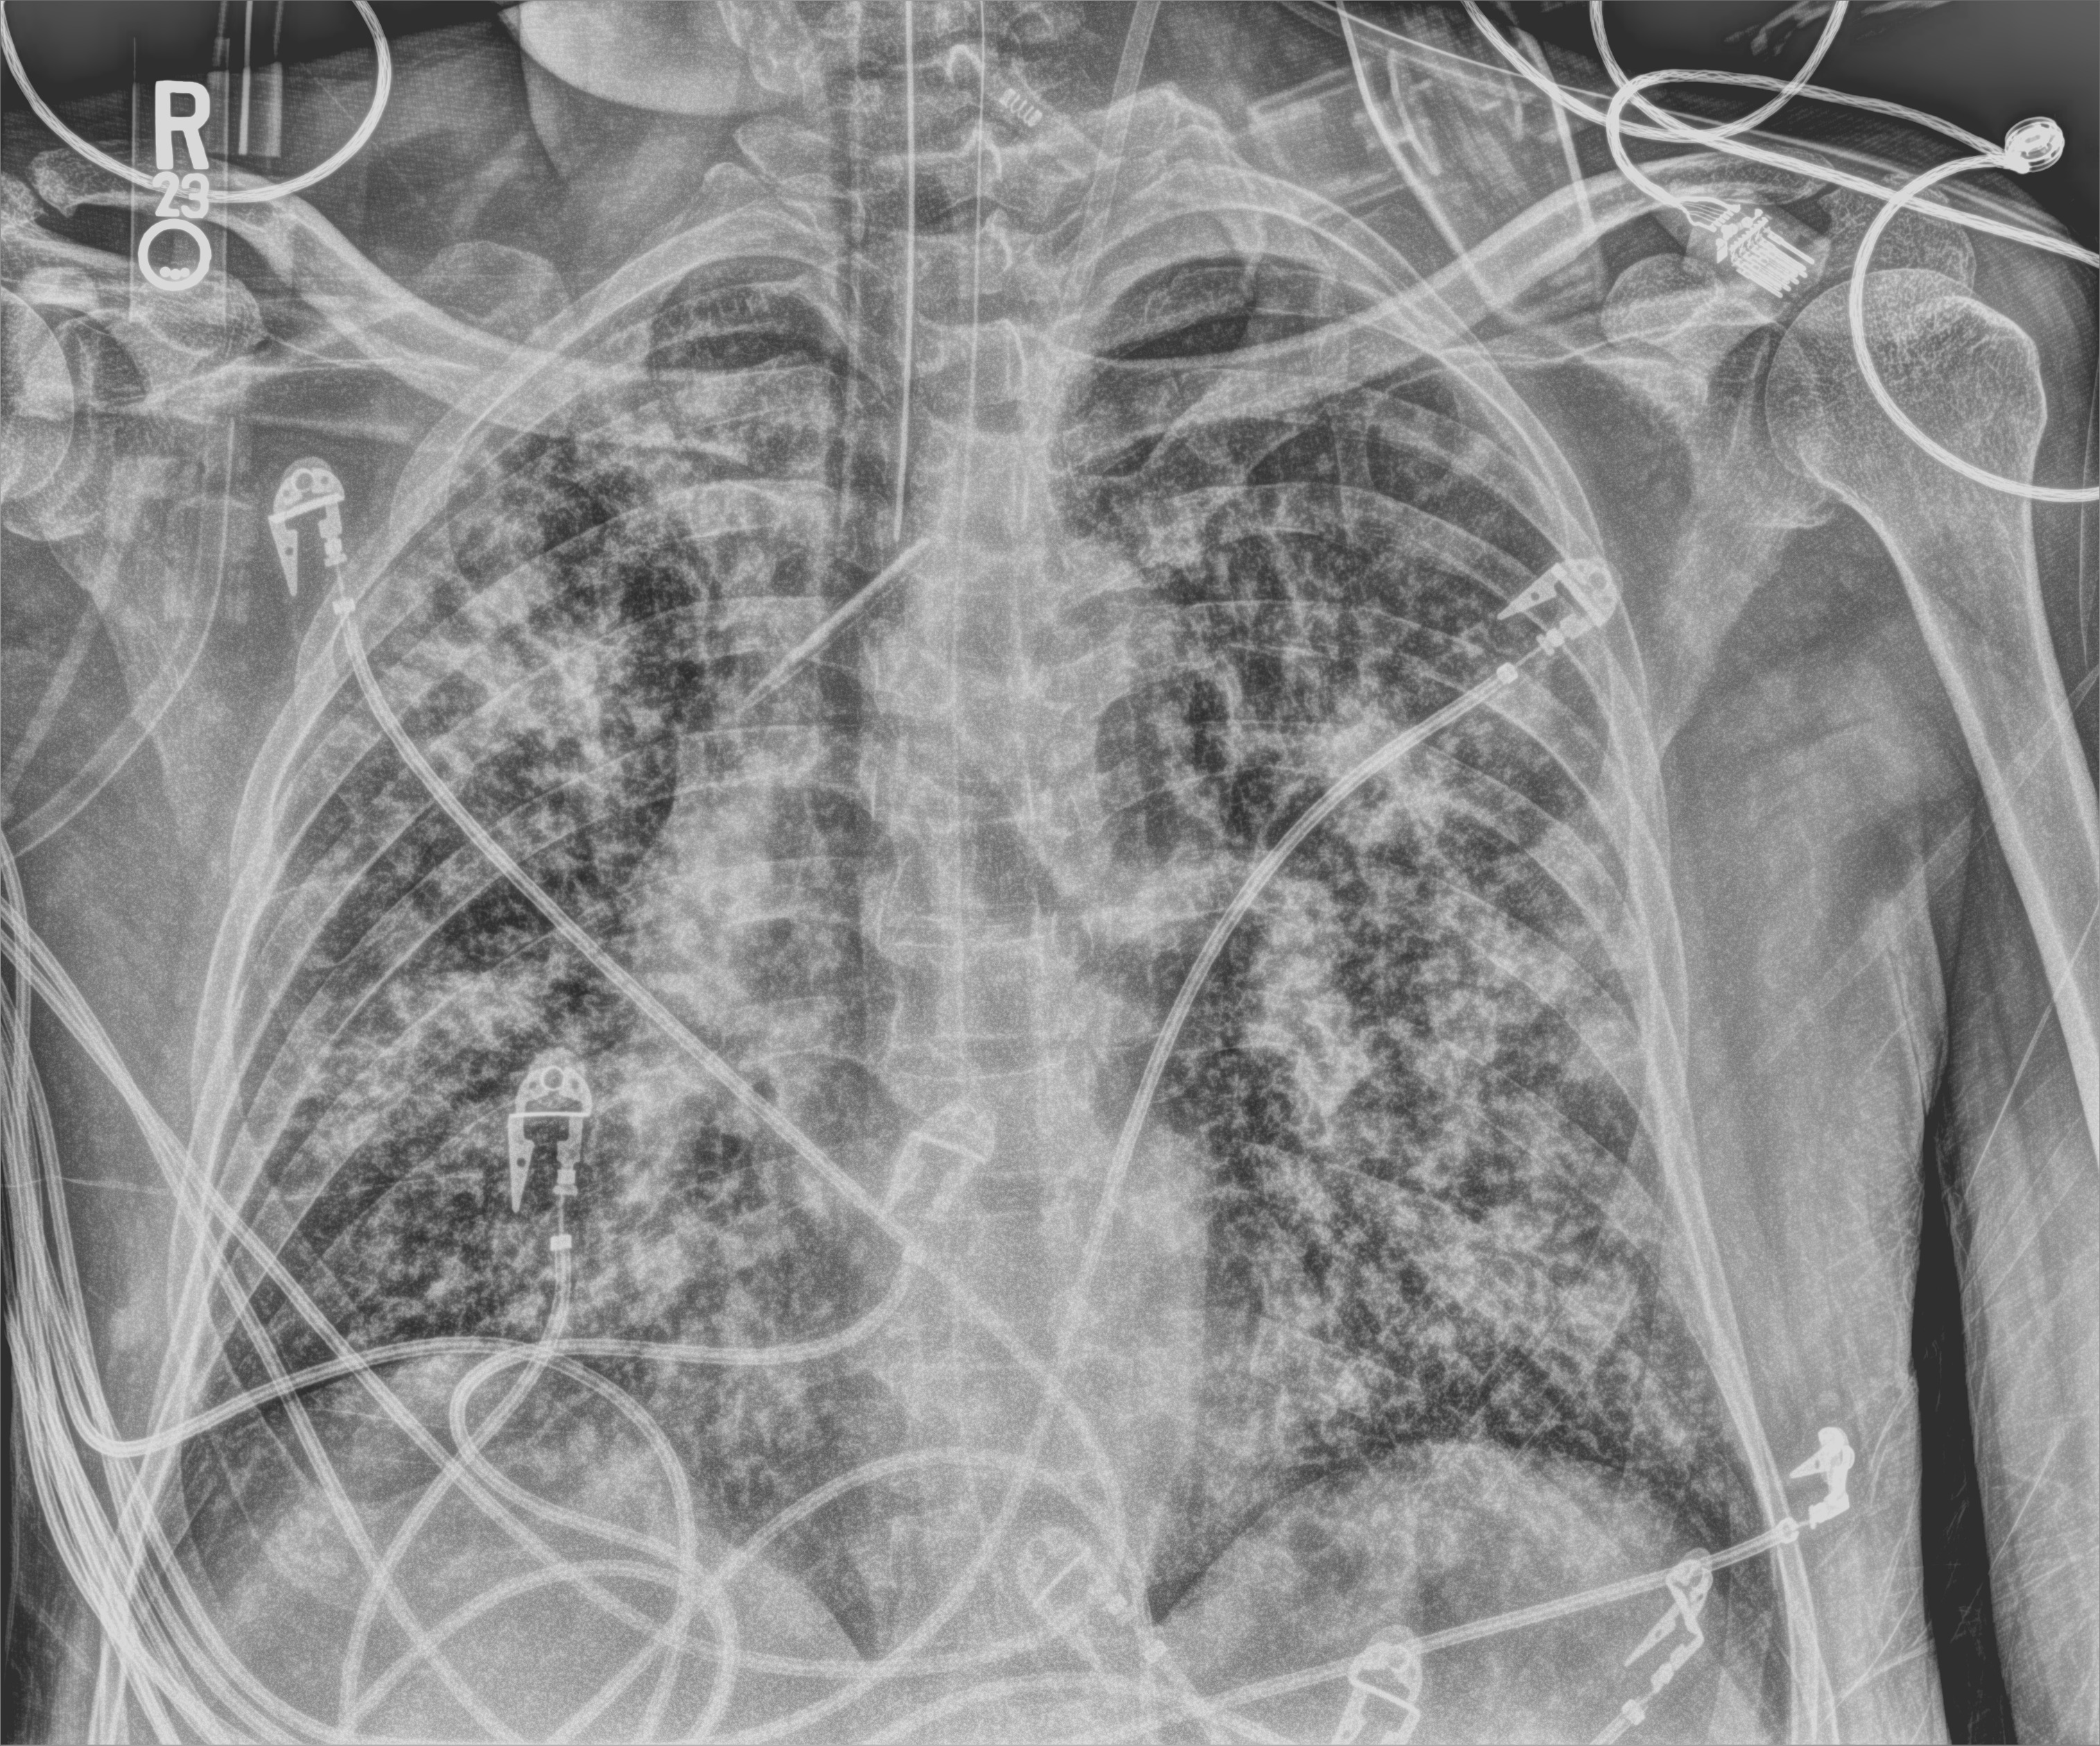
Portable chest radiograph, anteroposterior (AP) projection. Male patient hospitalised with COVID-19, age 60–74 years.
Admission-level facts for this patient (not findings on this image; timing relative to this image not recorded):
- admitted to intensive care during this hospital stay: yes
- mechanically ventilated during this hospital stay: yes
- length of hospital stay: 6 days